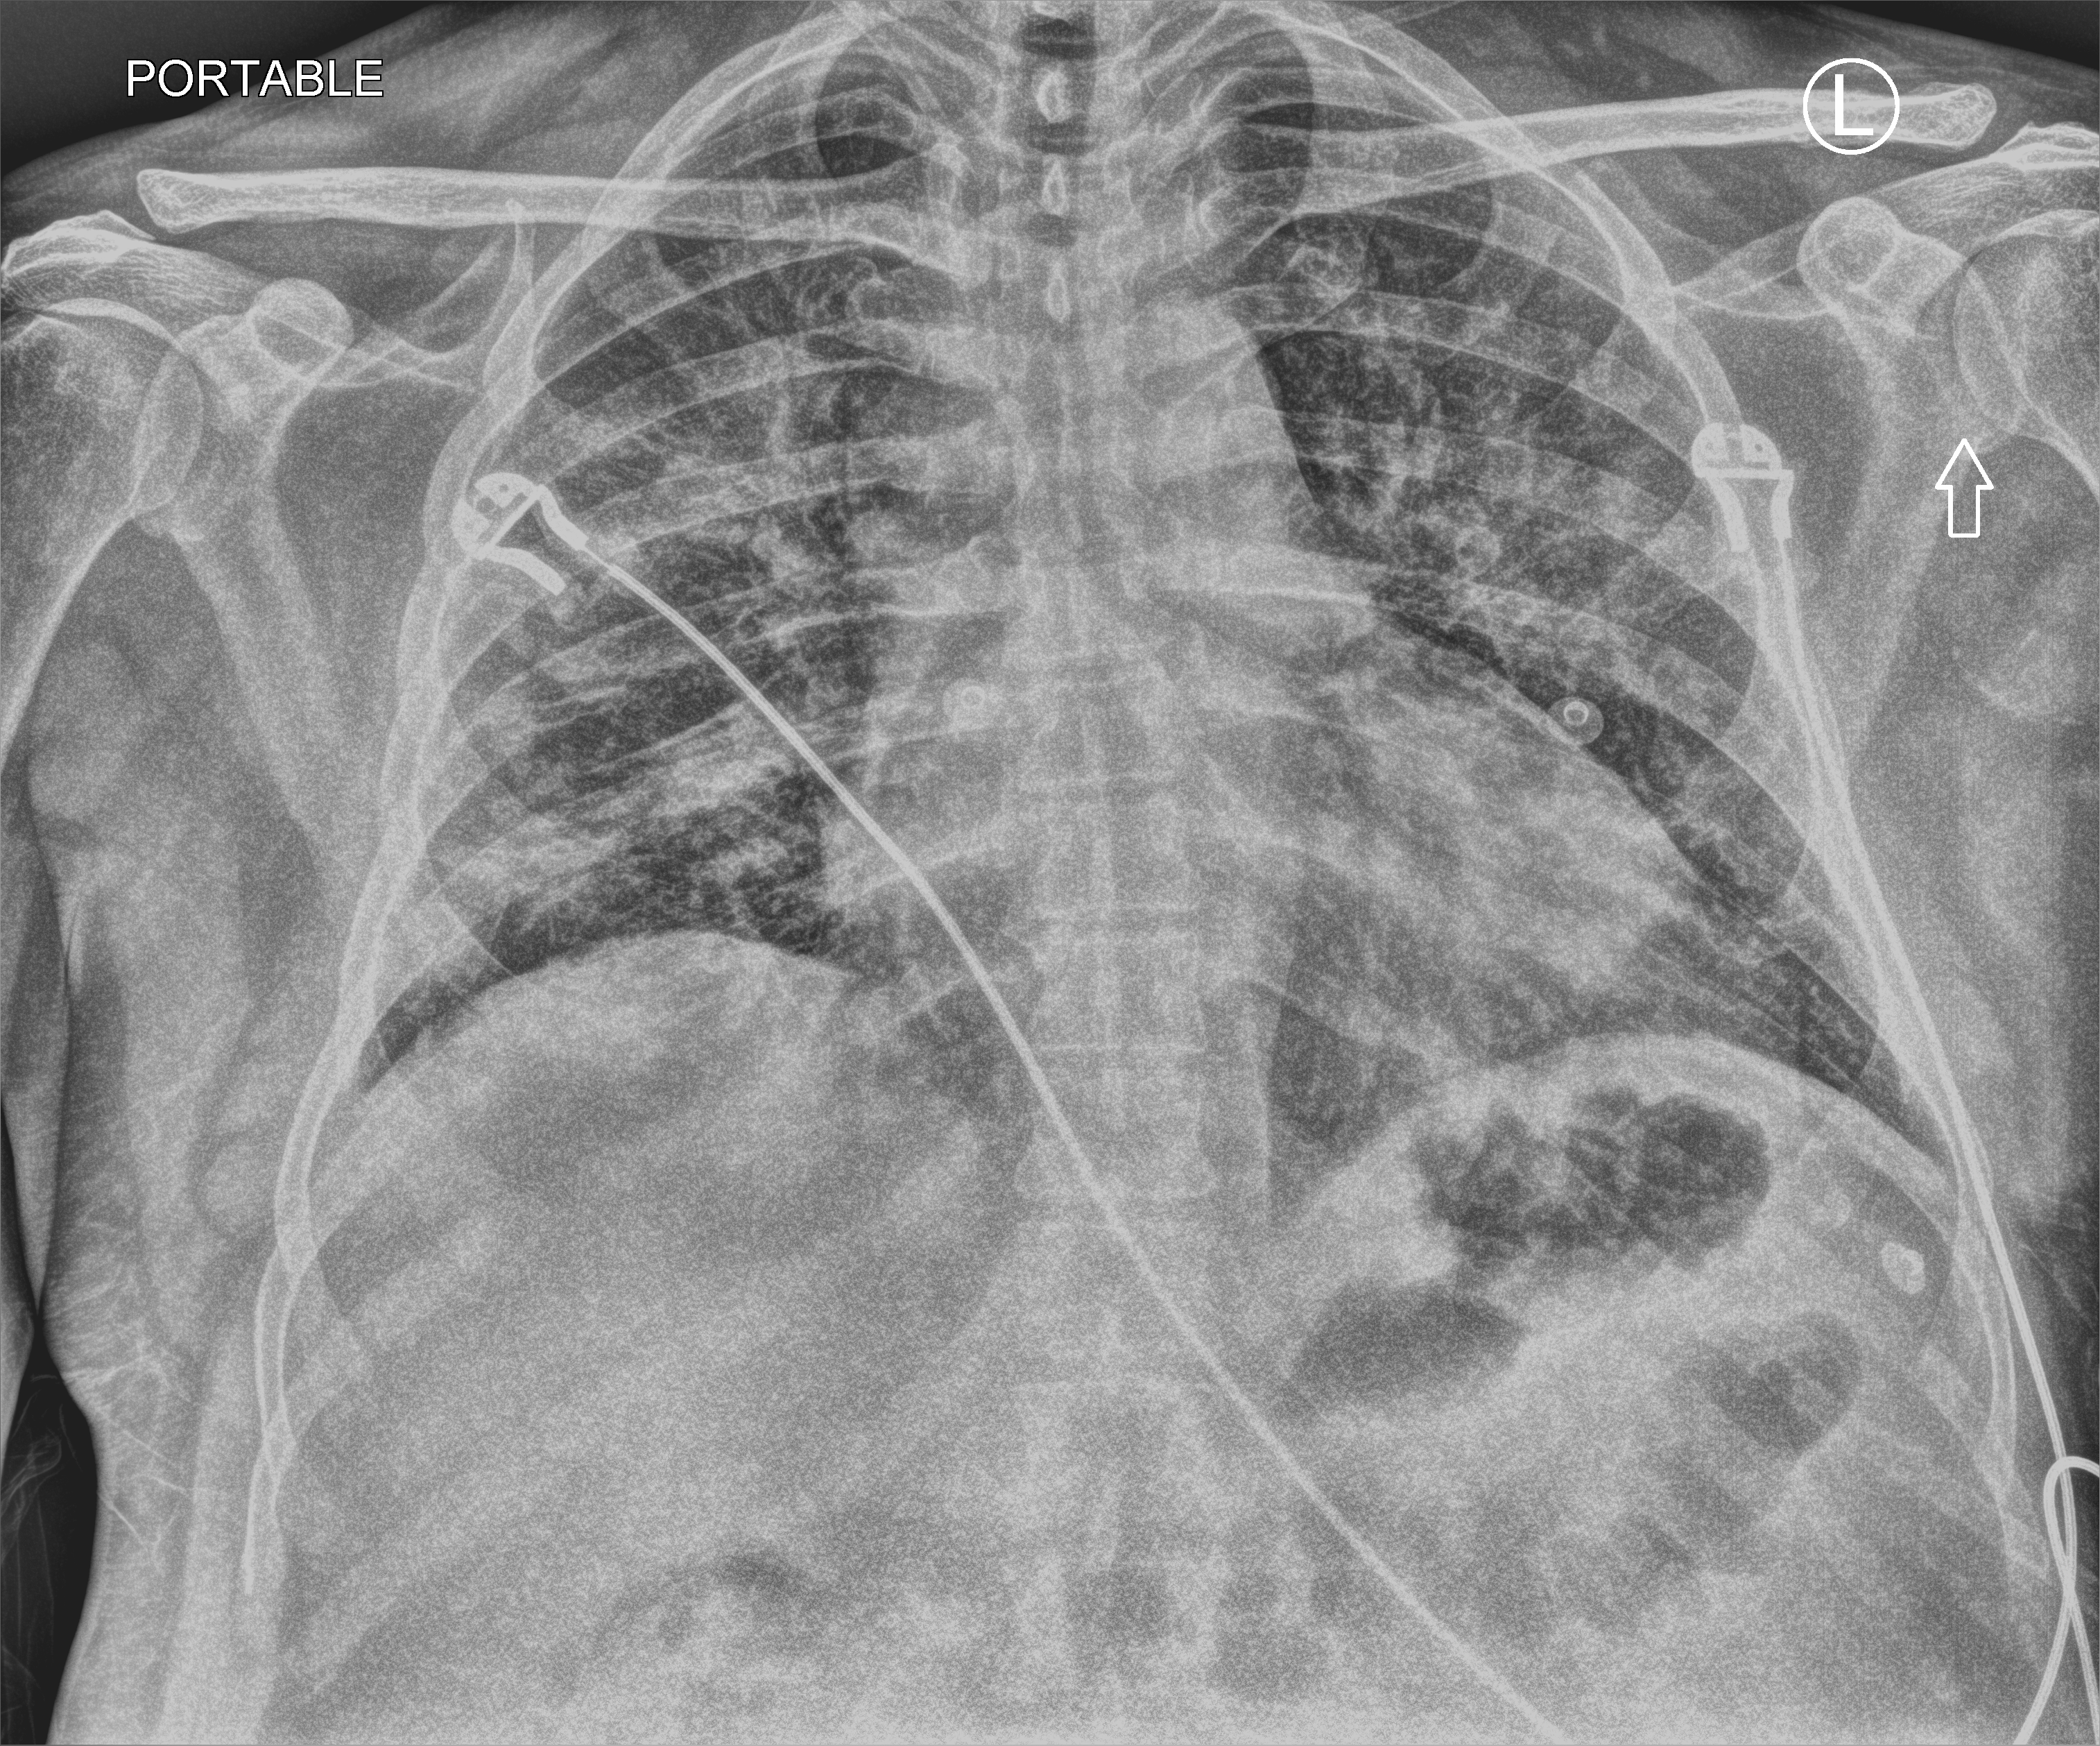
Portable chest radiograph; anteroposterior (AP) projection. Patient hospitalised with COVID-19; male, aged 18–59 years.
Admission-level facts for this patient (not findings on this image; timing relative to this image not recorded): COPD (admission record): no; mechanically ventilated during this hospital stay: no.